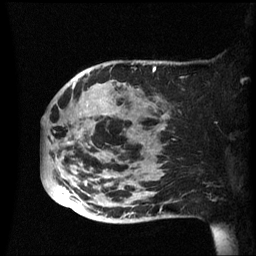
Breast MRI (dynamic contrast-enhanced), one sagittal slice; dynamic contrast-enhanced series, image 2 of 3 at this slice position (ordered by acquisition); 1.5 T; TE 4.2 ms, TR 8.4 ms; 2.4 mm slice thickness; 256 × 256 image matrix. Patient: female, 49 years.
Outlined on this slice (semi-automatically segmented with operator editing):
- analysis volume of interest (the breast-tissue region the enhancement analysis was run in; not a lesion): bounding box [x1, y1, x2, y2] px = [41, 60, 174, 223]
- tumour enhancement mask (voxels above the 70 % enhancement threshold inside the analysis volume of interest): [73, 68, 164, 220]